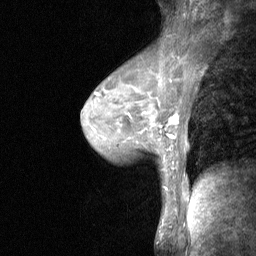
Breast MRI (dynamic contrast-enhanced), one sagittal slice. Position 39 of 64 along the scan axis. Dynamic contrast-enhanced study with each time point stored as its own series, time point 2 of 3 at this slice position (early post-contrast, ordered by acquisition time). 1.5 T. TE 4.8 ms, TR 27 ms. 2 mm slice thickness. 256 × 256 image matrix, field of view 200 × 200 mm. Female patient, age 44 years. From the clinical record (not read from this slice): setting: breast cancer imaged before/during neoadjuvant chemotherapy; receptor status: HR-positive, HER2-negative.
Outlined on this slice (semi-automatically segmented with operator editing):
- analysis volume of interest (the breast-tissue region the enhancement analysis was run in; not a lesion): bounding box [x1, y1, x2, y2] px = [140, 109, 180, 148]
- tumour enhancement mask (voxels above the 90 % enhancement threshold inside the analysis volume of interest): [169, 114, 179, 138]